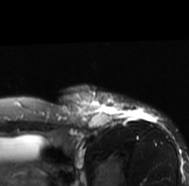
MRI of an extremity soft-tissue mass, one axial slice; slice 58 of 77 in the series (ordered by position); T2-weighted fat-saturated; MR volume resampled by the dataset authors to the PET/CT grid (not the native acquisition matrix); 3.27 mm slice thickness; 189 × 186 image matrix, field of view 185 × 182 mm. Female patient. From the clinical record (not read from this slice): histological type: leiomyosarcoma; grade: high; site of the primary tumour: groin.
Outlined on this slice (expert contour drawn on MRI and transferred to this co-registered scan by the dataset authors):
- gross tumour volume including surrounding oedema: box from (x=56, y=86) to (x=162, y=128) px
- gross tumour volume (mass): (x=65, y=91)–(x=109, y=128)